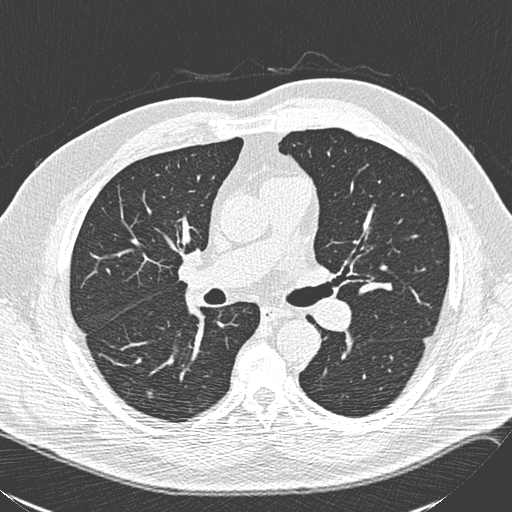
Low-dose screening chest CT, one axial slice. Slice 150 of 248 in the series (ordered by position). Lung window (W 1500 / L -600 HU). 1.3 mm slice thickness. 512 × 512 image matrix, field of view 357 × 357 mm.
Outlined on this slice (manually delineated by an expert):
- lesion 1 (tumor, lower lobe of right lung): bounding box [x1, y1, x2, y2] px = [148, 392, 153, 398]